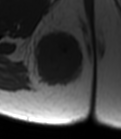
MRI of an extremity soft-tissue mass, one axial slice. MR volume resampled by the dataset authors to the PET/CT grid (not the native acquisition matrix). 3.27 mm slice thickness. 121 × 139 image matrix, field of view 118 × 136 mm. Female patient. From the clinical record (not read from this slice): histological type: epithelioid sarcoma; grade: intermediate; site of the primary tumour: right buttock.
Structures marked on this image (expert contour drawn on MRI and transferred to this co-registered scan by the dataset authors):
- gross tumour volume including surrounding oedema: box from (x=29, y=29) to (x=83, y=87) px
- gross tumour volume (mass): (x=34, y=32)–(x=83, y=85)